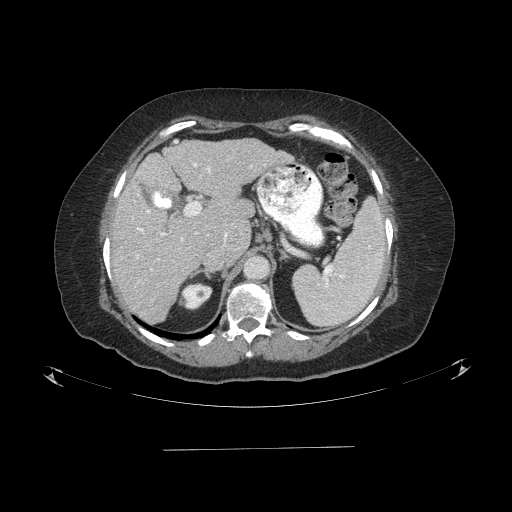
Contrast-enhanced abdominal CT (liver protocol), one axial slice; position 55 of 103 along the scan axis; reconstruction kernel STANDARD; 120 kVp; one of 2 acquisitions stored at this slice position; soft-tissue window (W 400 / L 40 HU); 512 × 512 image matrix. From the clinical record (not read from this slice): diagnosis: hepatocellular carcinoma (patient treated with transarterial chemoembolisation; whether this scan precedes or follows treatment is not stated here); TNM stage (as recorded): Stage-IIIA; Child-Pugh class: A.
Annotated regions visible in this slice (semi-automatically segmented with operator editing):
- liver parenchyma outside the tumour (the mass and vessels are separate outlines, so this box may not span the whole liver): bounding box [x1, y1, x2, y2] px = [112, 138, 286, 322]
- liver vessels: [137, 163, 252, 258]